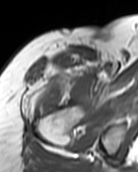
MRI of an extremity soft-tissue mass, one axial slice; position 86 of 99 along the scan axis; MR volume resampled by the dataset authors to the PET/CT grid (not the native acquisition matrix); 3.27 mm slice thickness; 138 × 172 image matrix, field of view 135 × 168 mm. Female patient. Case-level facts recorded for this patient, not image findings: histological type: pleiomorphic undifferentiated sarcoma; grade: high; site of the primary tumour: right quadricep.
Structures marked on this image (expert contour drawn on MRI and transferred to this co-registered scan by the dataset authors):
- gross tumour volume including surrounding oedema: box from (x=35, y=82) to (x=58, y=115) px